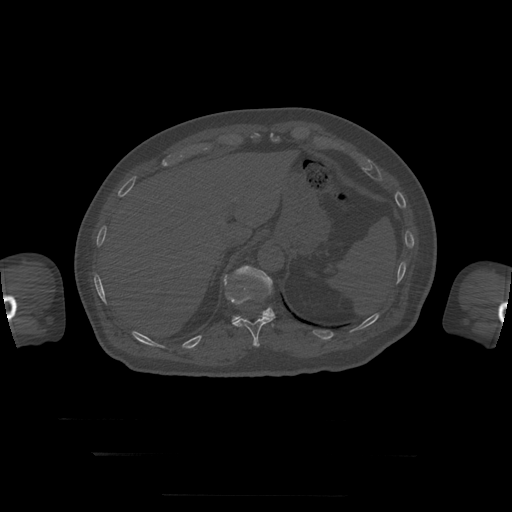
CT including the spine, one axial slice; reconstruction kernel STANDARD; 120 kVp; bone window (W 1800 / L 400 HU); 1.25 mm slice thickness; 512 × 512 image matrix. Patient age 73 years. From the clinical record (not read from this slice): primary cancer: prostate.
Structures marked on this image (semi-automatically segmented with operator editing):
- T11 vertebra: bounding box [x1, y1, x2, y2] px = [224, 275, 276, 347]
- T12 vertebra: [232, 266, 275, 323]